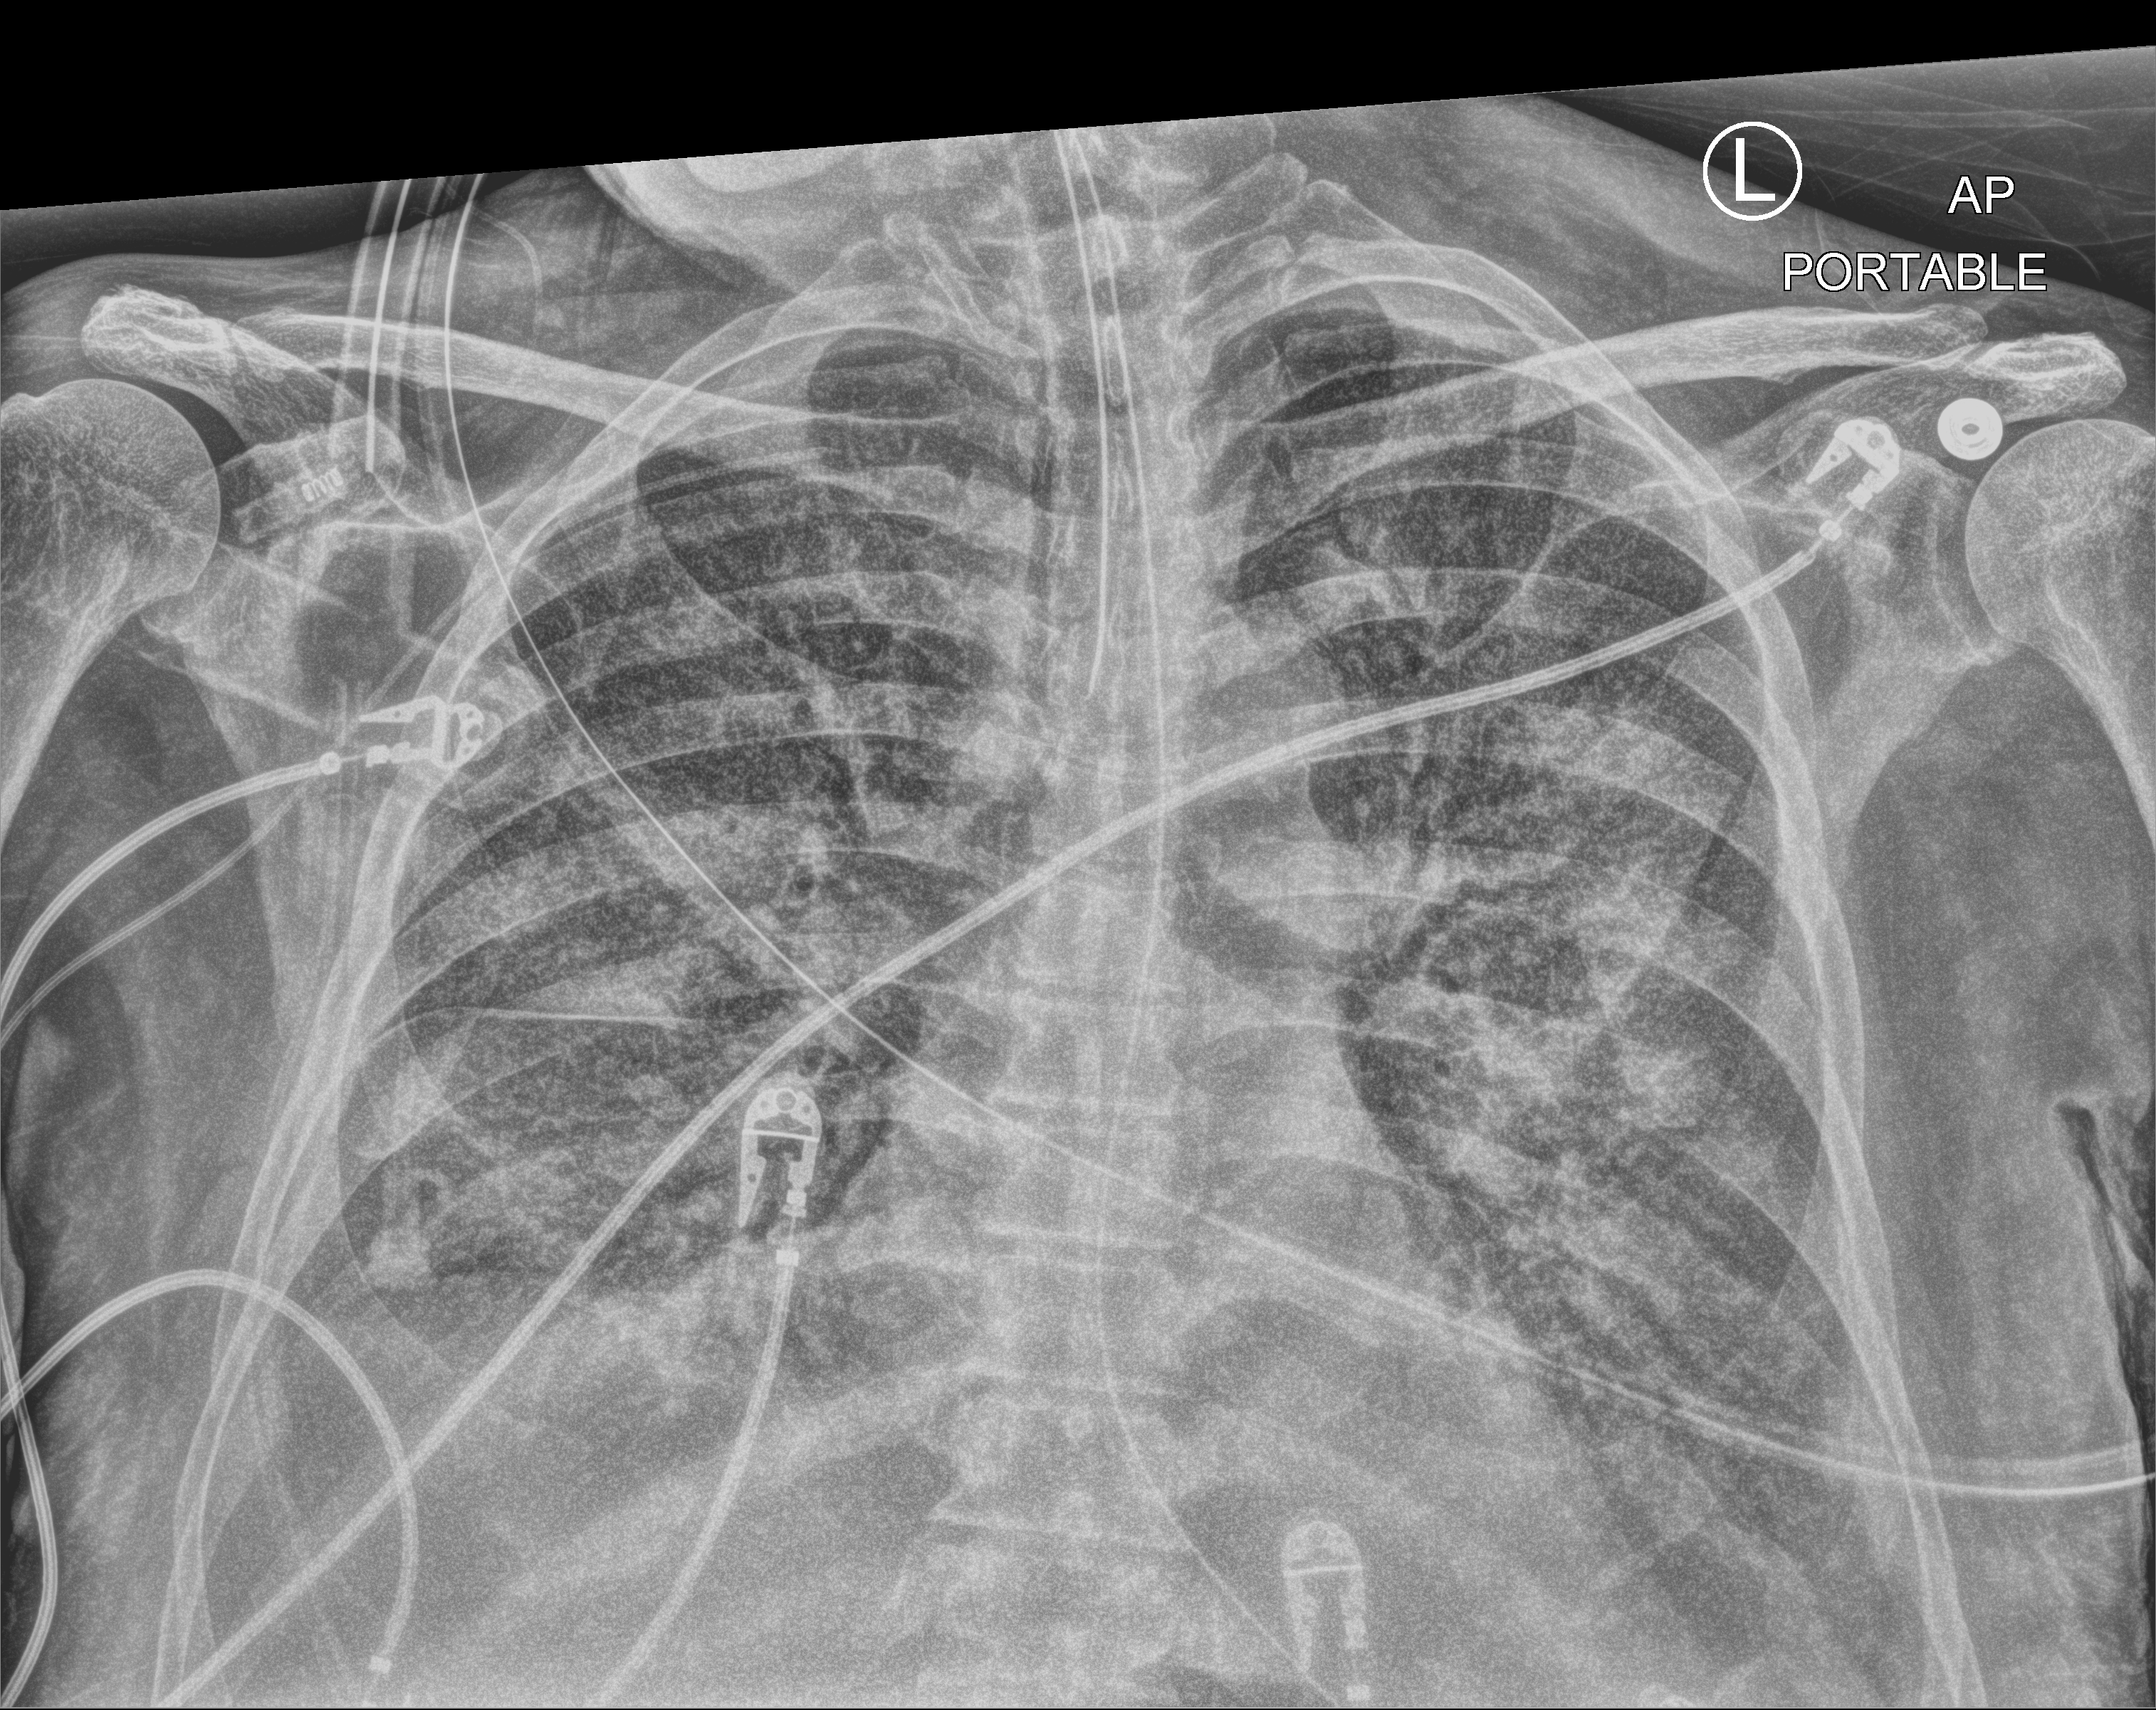
Bedside chest radiograph (computed radiography); anteroposterior (AP) projection. Patient hospitalised with COVID-19; male, aged 60–74 years.
From the hospital-stay record, not from the radiograph (when in the stay this image was taken is not recorded):
- smoking status (admission record): former
- length of hospital stay: 24 days